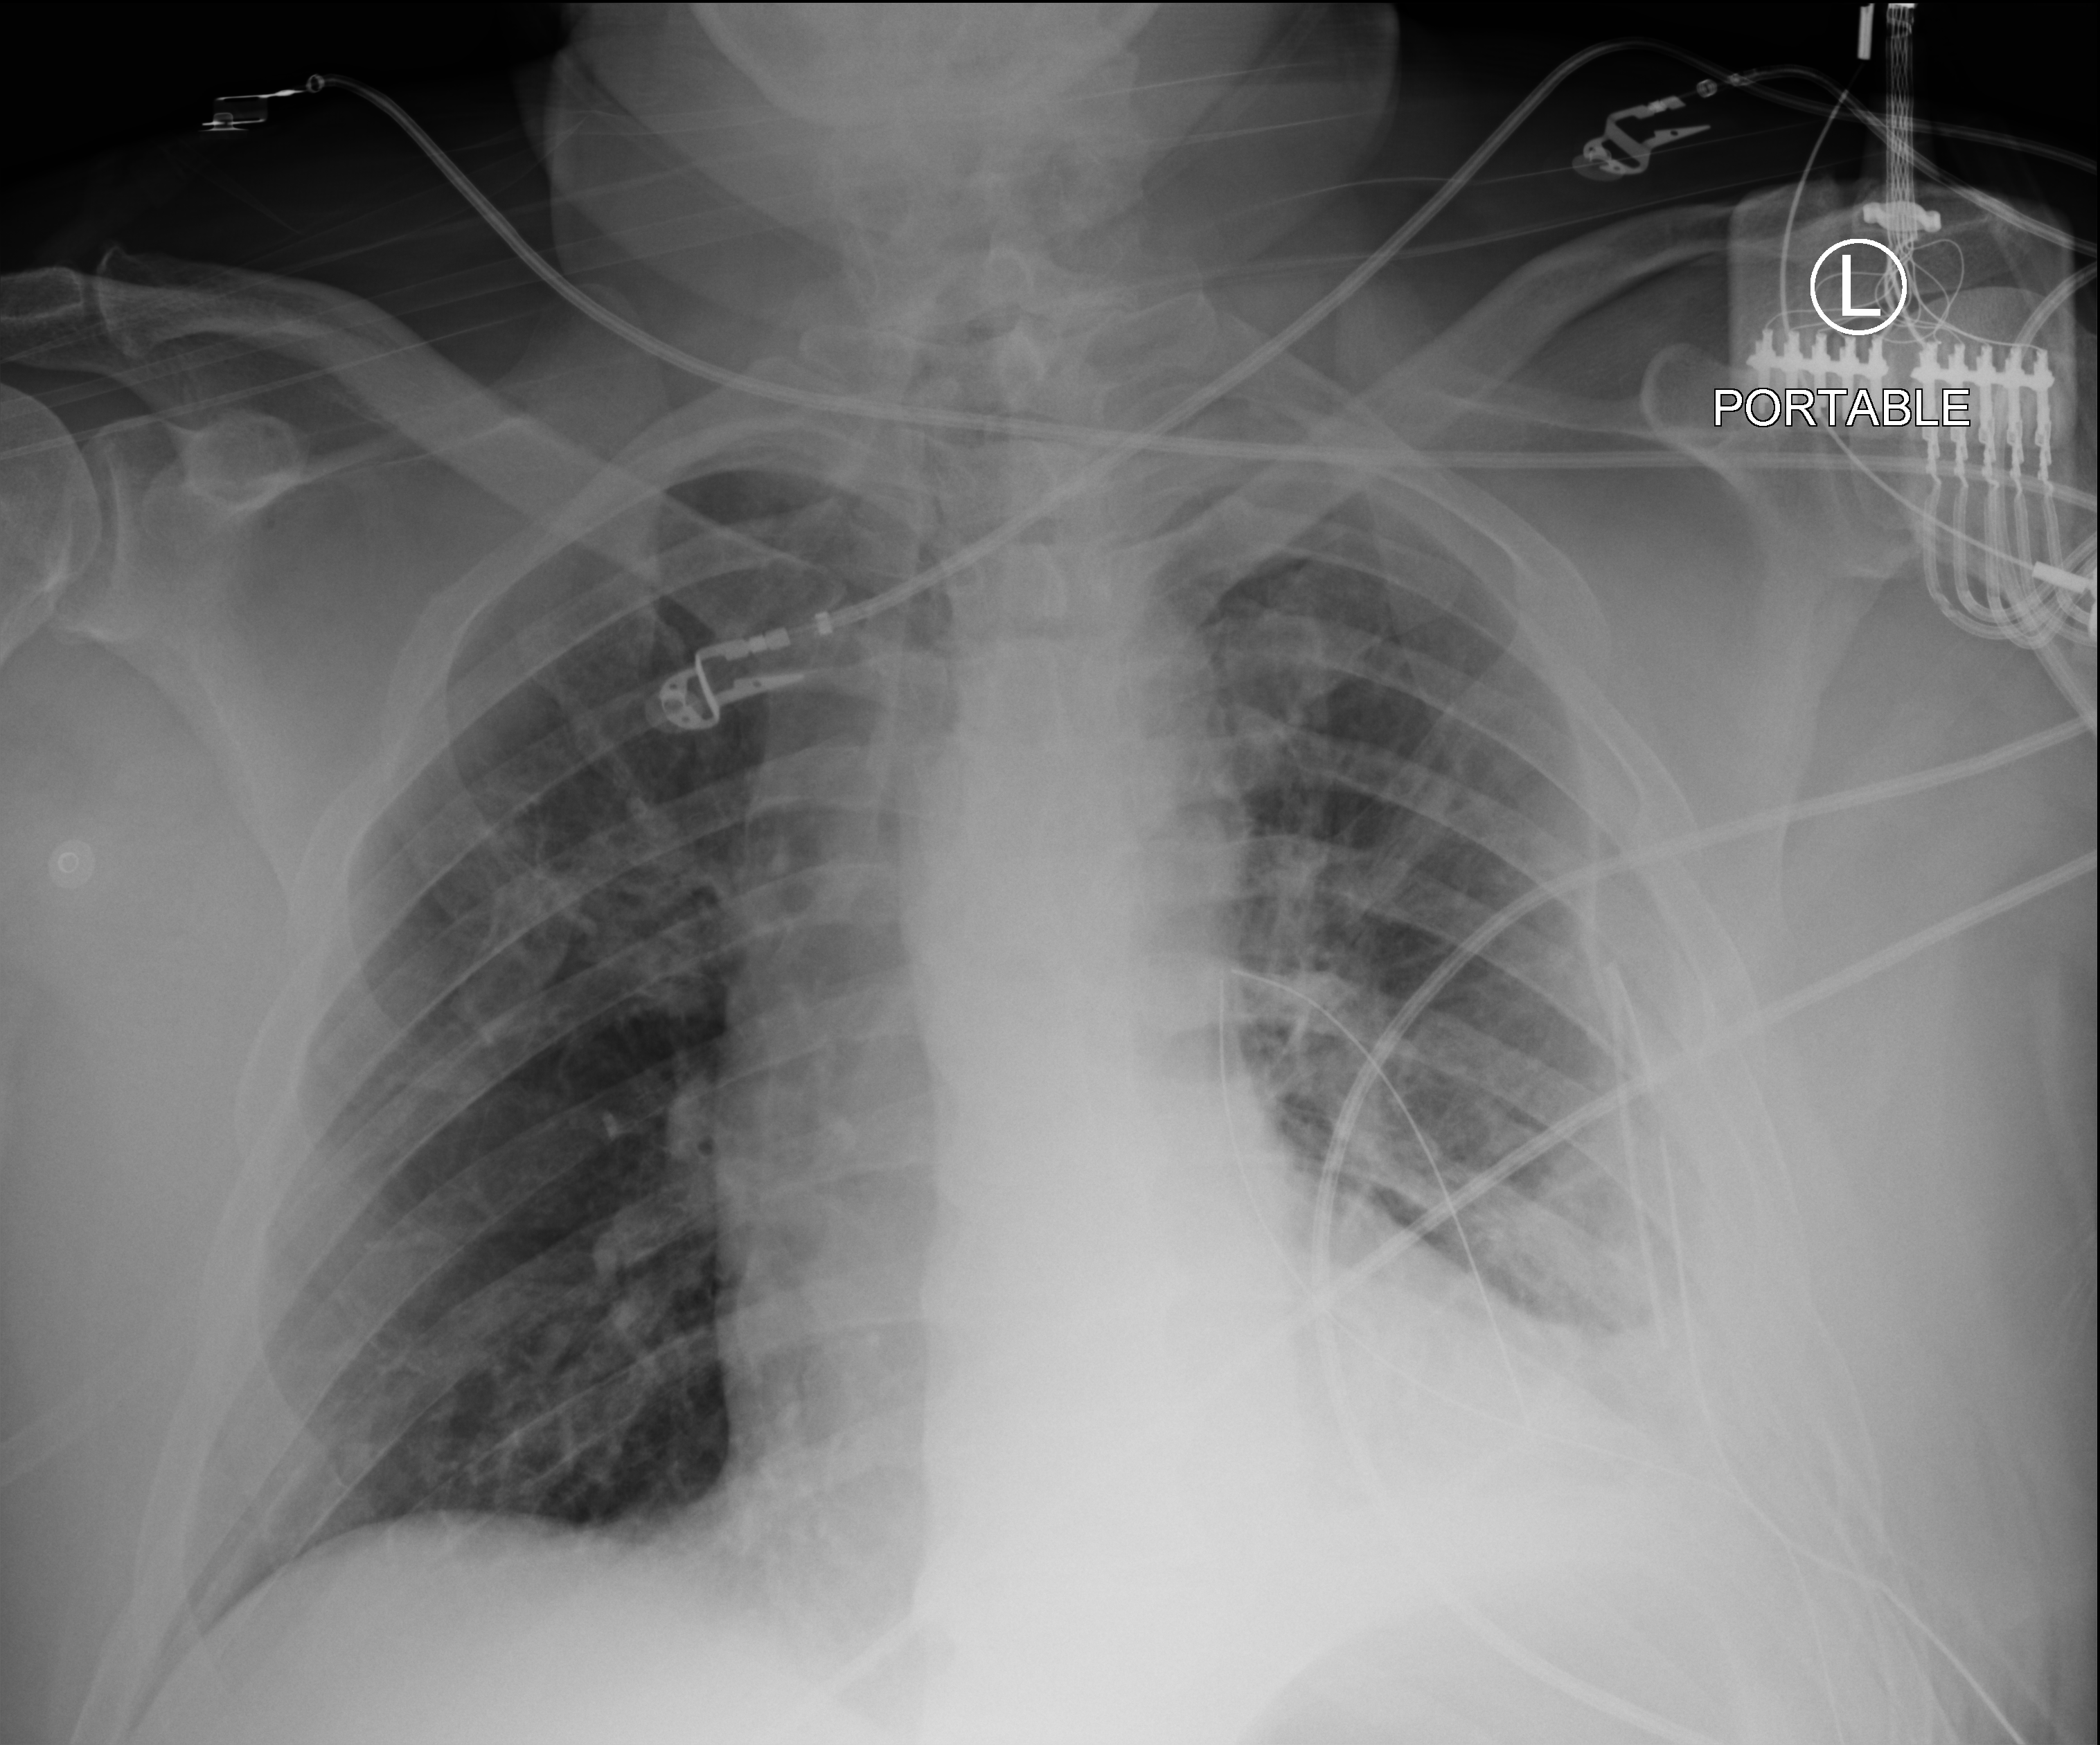
Portable chest radiograph. Patient hospitalised with COVID-19; male, aged 18–59 years.
Admission-level facts for this patient (not findings on this image; timing relative to this image not recorded):
- mechanically ventilated during this hospital stay: no